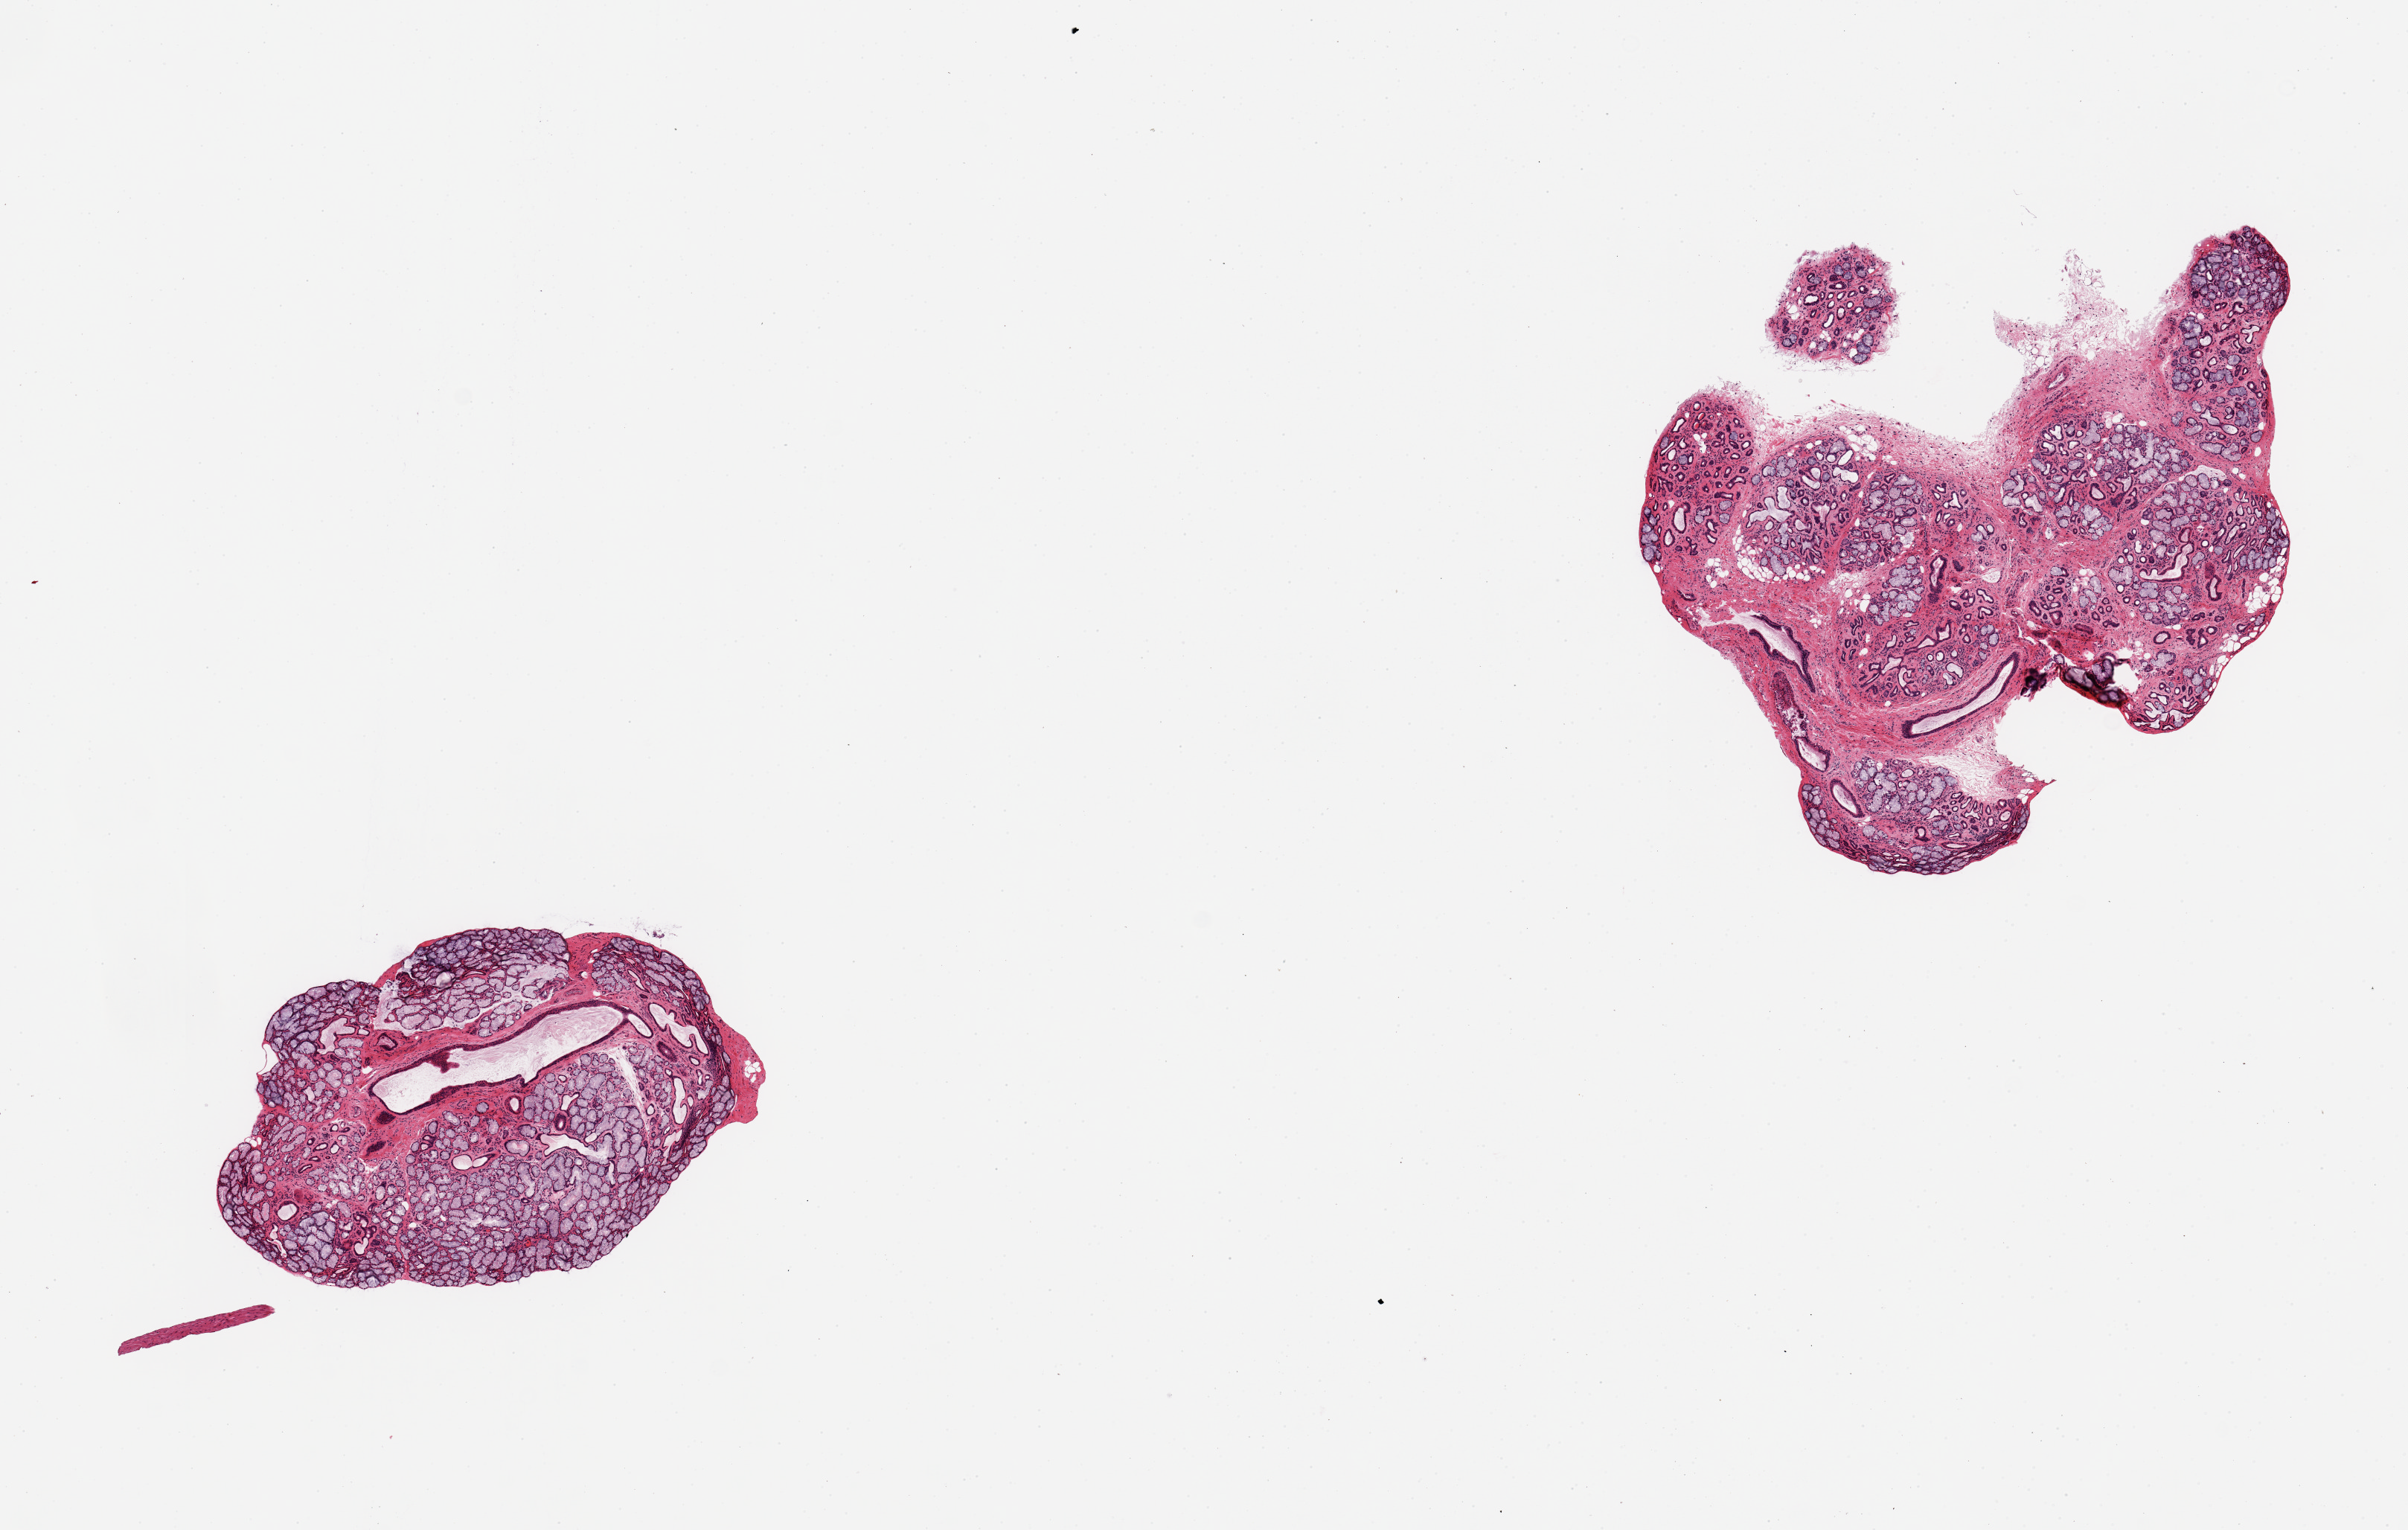
Hematoxylin and eosin (H&E) whole-slide image, low-resolution overview of the scanned area, about 12.8 x 8.1 mm (acquisition: 20x scan); PAXgene-fixed, paraffin-embedded tissue; target tissue: minor salivary gland; tissue donor sample. Female donor.
Reviewer comment on this tissue sample: 2 pieces, glandular elements ~80% of specimen; good specimen.